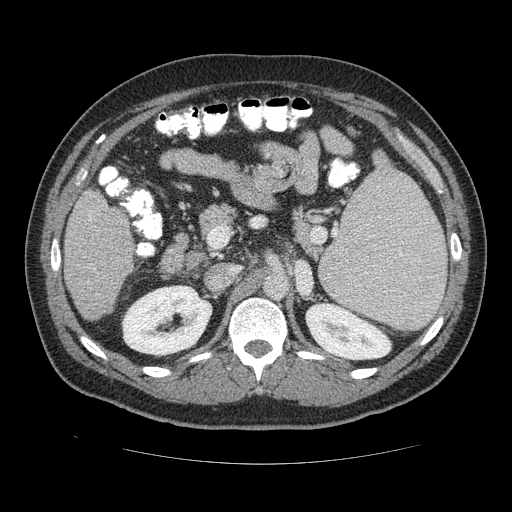
Contrast-enhanced abdominal CT (liver protocol), one axial slice. Position 63 of 113 along the scan axis. Reconstruction kernel STANDARD. 120 kVp. Soft-tissue window (W 400 / L 40 HU). 2.5 mm slice thickness. 512 × 512 image matrix, field of view 400 × 400 mm. Case-level facts recorded for this patient, not image findings: diagnosis: hepatocellular carcinoma (patient treated with transarterial chemoembolisation; whether this scan precedes or follows treatment is not stated here); TNM stage (as recorded): Stage-II.
Annotated regions visible in this slice (semi-automatically segmented with operator editing):
- liver parenchyma outside the tumour (the mass and vessels are separate outlines, so this box may not span the whole liver): bounding box <62,184,138,322> (left, top, right, bottom; pixels)
- liver vessels: <87,218,132,272>